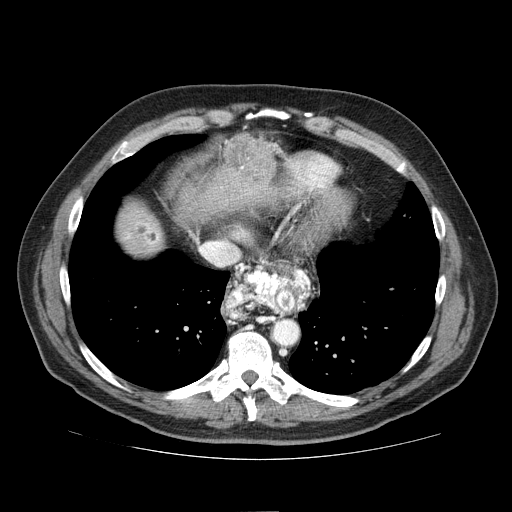
Contrast-enhanced abdominal CT (liver protocol), one axial slice. Position 68 of 81 along the scan axis. 100 kVp. One of 2 acquisitions stored at this slice position. Soft-tissue window (W 400 / L 40 HU). 2.5 mm slice thickness. 512 × 512 image matrix, field of view 400 × 400 mm. Case-level facts recorded for this patient, not image findings: diagnosis: hepatocellular carcinoma (patient treated with transarterial chemoembolisation; whether this scan precedes or follows treatment is not stated here); TNM stage (as recorded): Stage-IIIA.
Structures marked on this image (semi-automatically segmented with operator editing):
- liver parenchyma outside the tumour (the mass and vessels are separate outlines, so this box may not span the whole liver): box from (x=118, y=157) to (x=275, y=254) px
- mass: (x=226, y=134)–(x=276, y=184)
- liver vessels: (x=127, y=223)–(x=159, y=244)